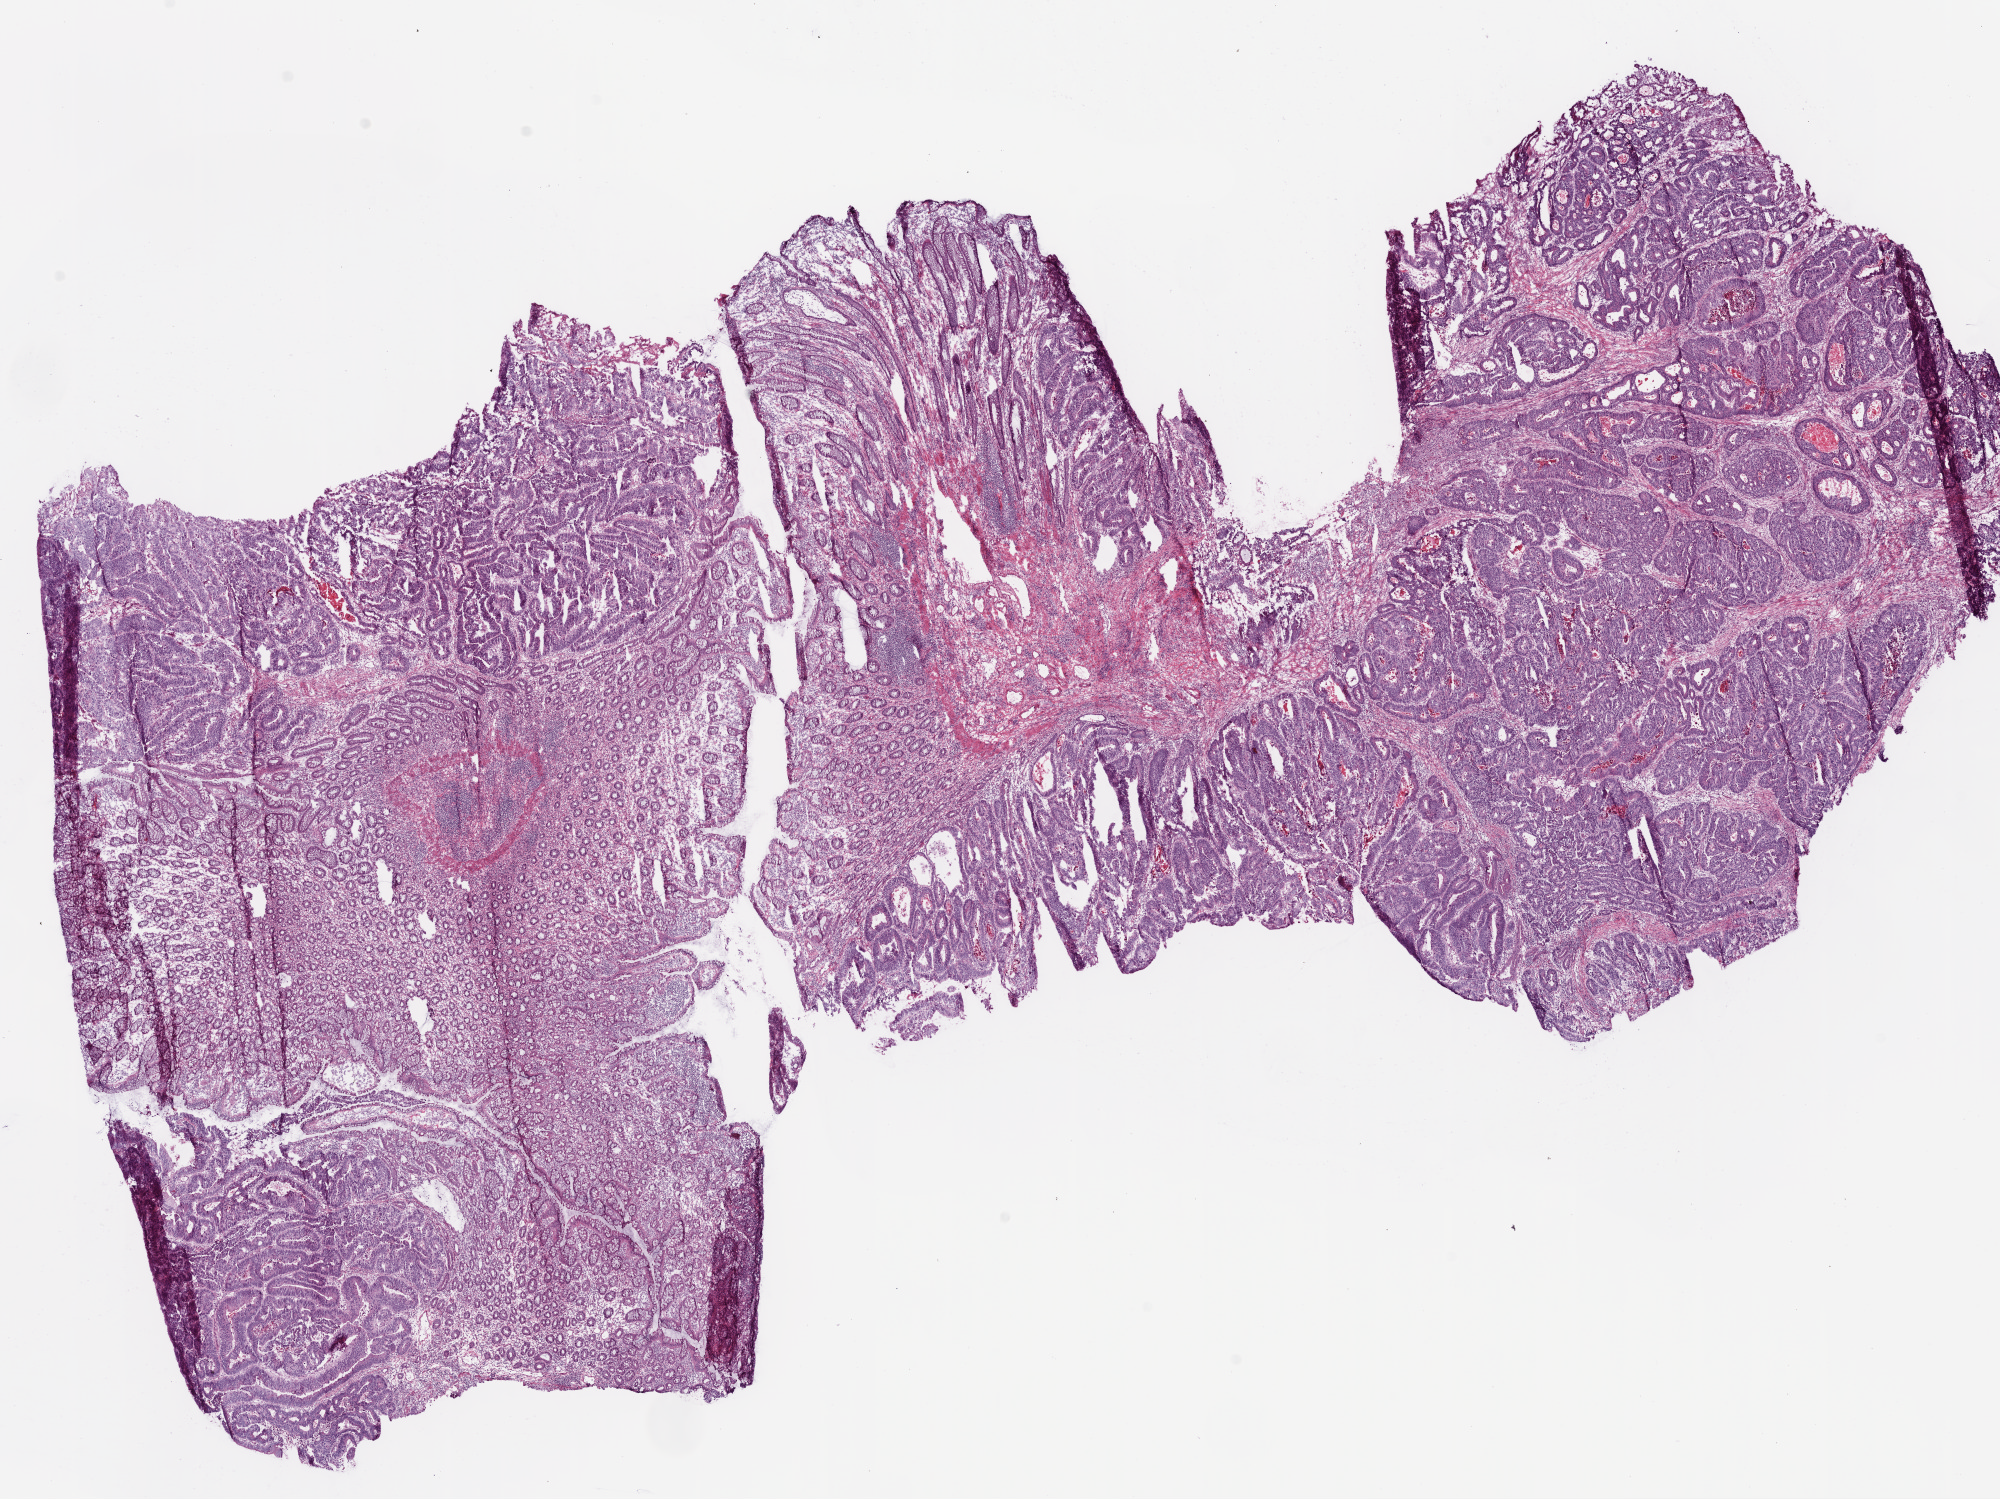
H&E-stained whole-slide image — shown as a low-resolution overview of the whole scanned area (about 16.0 x 12.0 mm). Frozen section from the bottom of the tissue portion. Colon, primary tumour sample. Male patient; age at initial diagnosis 77 years.
Pathologic diagnosis: Adenocarcinoma, NOS.